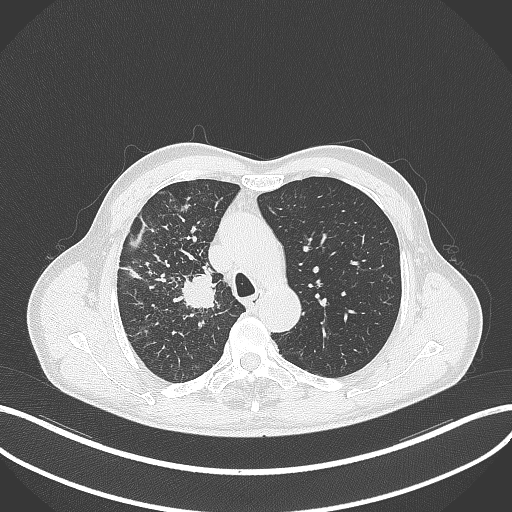
Chest CT, one axial slice; slice 350 of 490 in the series (ordered by position); 120 kVp; lung window (W 1500 / L -600 HU); 512 × 512 image matrix. Male patient, age 69 years. From the clinical record (not read from this slice): clinical TNM (as recorded): T2a N0 M0.
Structures marked on this image (bounding box drawn by a radiologist):
- lung tumour (recorded histology: adenocarcinoma): bounding box (x1, y1, x2, y2) in pixels: (180, 270, 222, 315)